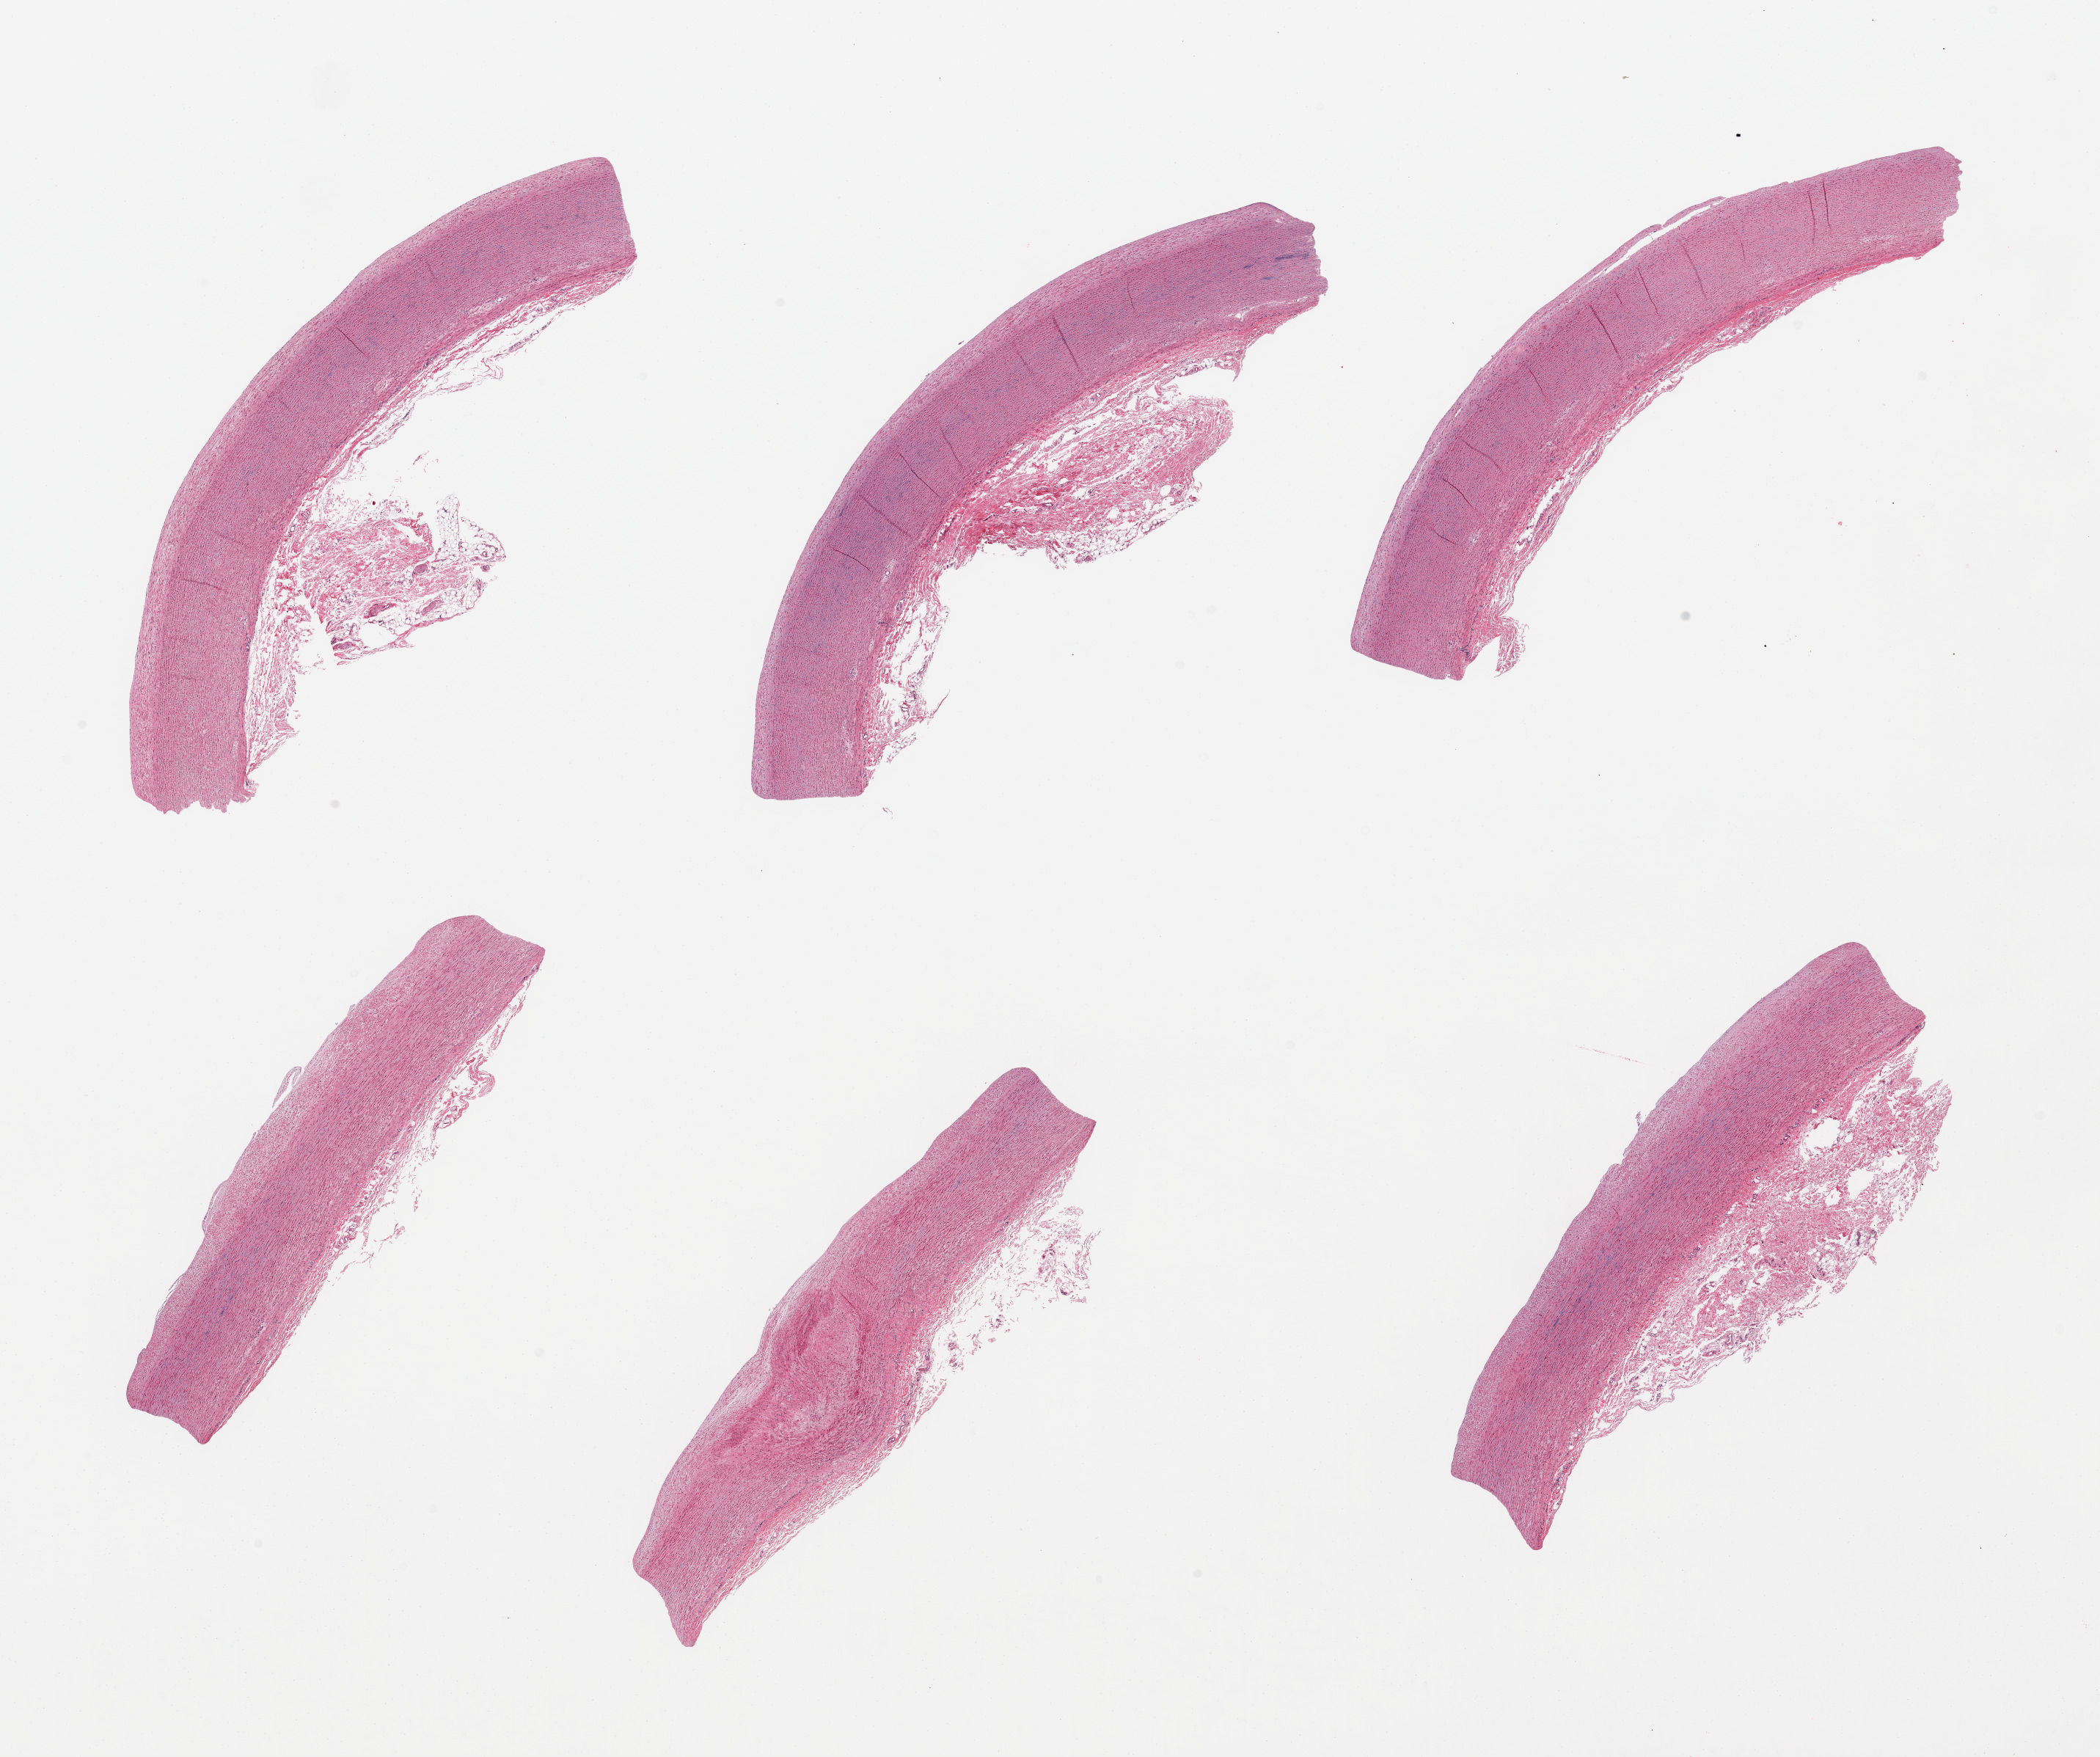
Hematoxylin and eosin (H&E) whole-slide image, brightfield — whole scanned area (about 22.6 x 18.9 mm, slide scanned at 20x) shown as a low-resolution overview; PAXgene-fixed paraffin-embedded (PFPE) section; section of aorta (target tissue); donor tissue sample. Donor sex: female.
• review note (as recorded): 6 pieces, atherosis up to ~0.2mm